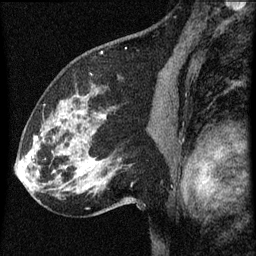
Breast MRI (dynamic contrast-enhanced), one sagittal slice; position 40 of 60 along the scan axis; dynamic contrast-enhanced series, image 2 of 3 at this slice position (ordered by acquisition); 1.5 T; TE 4.2 ms, TR 8 ms; 2 mm slice thickness; 256 × 256 image matrix, field of view 180 × 180 mm. Female patient, age 61 years.
Annotated regions visible in this slice (semi-automatic segmentation, software-assisted and operator-edited):
- analysis volume of interest (the breast-tissue region the enhancement analysis was run in; not a lesion): box from (x=27, y=82) to (x=136, y=209) px
- tumour enhancement mask (voxels above the 70 % enhancement threshold inside the analysis volume of interest): (x=32, y=156)–(x=34, y=159)